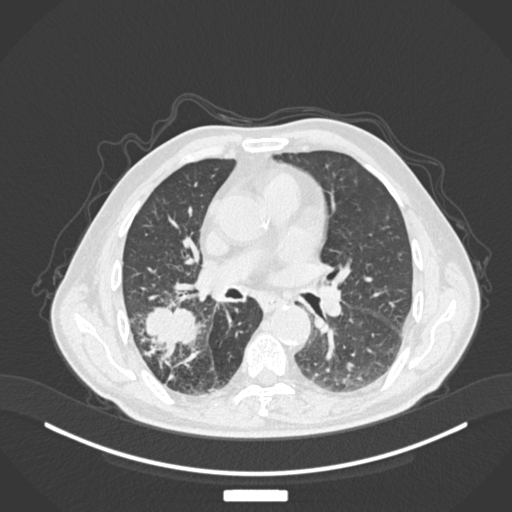
Chest CT, one axial slice; position 89 of 201 along the scan axis; 120 kVp; lung window (W 1500 / L -600 HU); 1 mm slice thickness; 512 × 512 image matrix, field of view 400 × 400 mm. Patient: male, 72 years. From the clinical record (not read from this slice): clinical TNM (as recorded): T3 N2 M0.
Outlined on this slice (rectangle marked by the reading radiologist):
- lung tumour (recorded histology: adenocarcinoma): box from (x=139, y=299) to (x=199, y=356) px